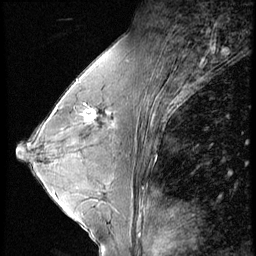
Breast MRI (dynamic contrast-enhanced), one sagittal slice. Position 35 of 56 along the scan axis. 4 images stored at this slice position (order not interpretable as contrast timing). 1.5 T. TE 4.2 ms, TR 9 ms. 2.5 mm slice thickness. 256 × 256 image matrix. Patient: female, 45 years. From the clinical record (not read from this slice): setting: breast cancer imaged before/during neoadjuvant chemotherapy; receptor status: triple-negative.
Annotated regions visible in this slice (semi-automatically segmented with operator editing):
- analysis volume of interest (the breast-tissue region the enhancement analysis was run in; not a lesion): bounding box <77,104,97,124> (left, top, right, bottom; pixels)
- tumour enhancement mask (voxels above the 140 % enhancement threshold inside the analysis volume of interest): <77,104,95,122>